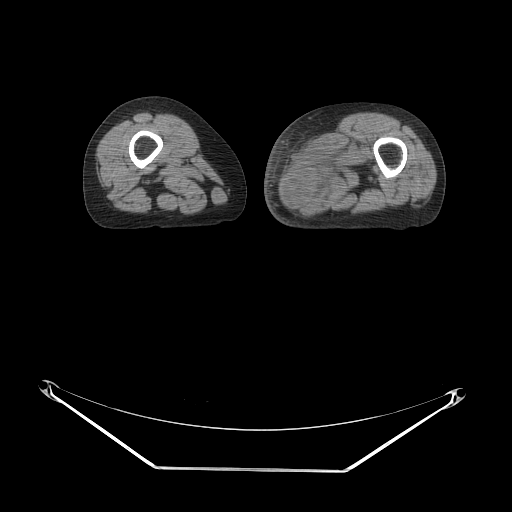
CT of an extremity soft-tissue mass (from a PET/CT study), one axial slice. Position 19 of 91 along the scan axis. 140 kVp. Soft-tissue window (W 400 / L 40 HU). 3.75 mm slice thickness. 512 × 512 image matrix, field of view 500 × 500 mm. Female patient. From the clinical record (not read from this slice): histological type: pleomorphic leiomyosarcoma; grade: high; site of the primary tumour: left thigh.
Structures marked on this image (expert contour drawn on MRI and transferred to this co-registered scan by the dataset authors):
- gross tumour volume including surrounding oedema: bounding box [x1, y1, x2, y2] px = [283, 132, 369, 207]
- gross tumour volume (mass): [283, 157, 339, 206]